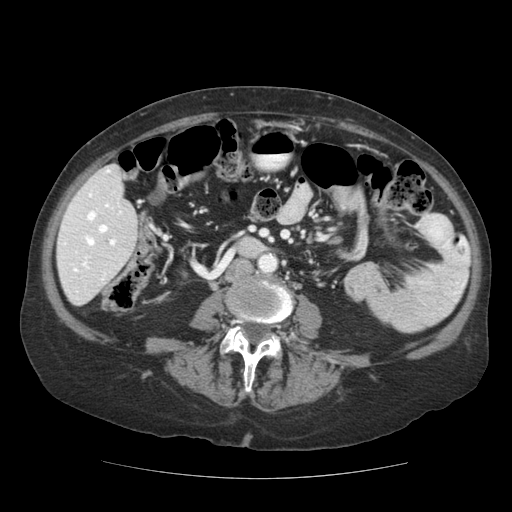
Contrast-enhanced abdominal CT (liver protocol), one axial slice; position 39 of 111 along the scan axis; reconstruction kernel STANDARD; 140 kVp; soft-tissue window (W 400 / L 40 HU); 2.5 mm slice thickness; 512 × 512 image matrix, field of view 360 × 360 mm. Case-level facts recorded for this patient, not image findings: diagnosis: hepatocellular carcinoma (patient treated with transarterial chemoembolisation; whether this scan precedes or follows treatment is not stated here); TNM stage (as recorded): Stage-I; Child-Pugh class: A; tumour nodularity: uninodular; tumour size: 7.3 cm.
Annotated regions visible in this slice (semi-automatically segmented with operator editing):
- liver parenchyma outside the tumour (the mass and vessels are separate outlines, so this box may not span the whole liver): bounding box [x1, y1, x2, y2] px = [56, 164, 138, 306]
- liver vessels: [63, 169, 122, 281]